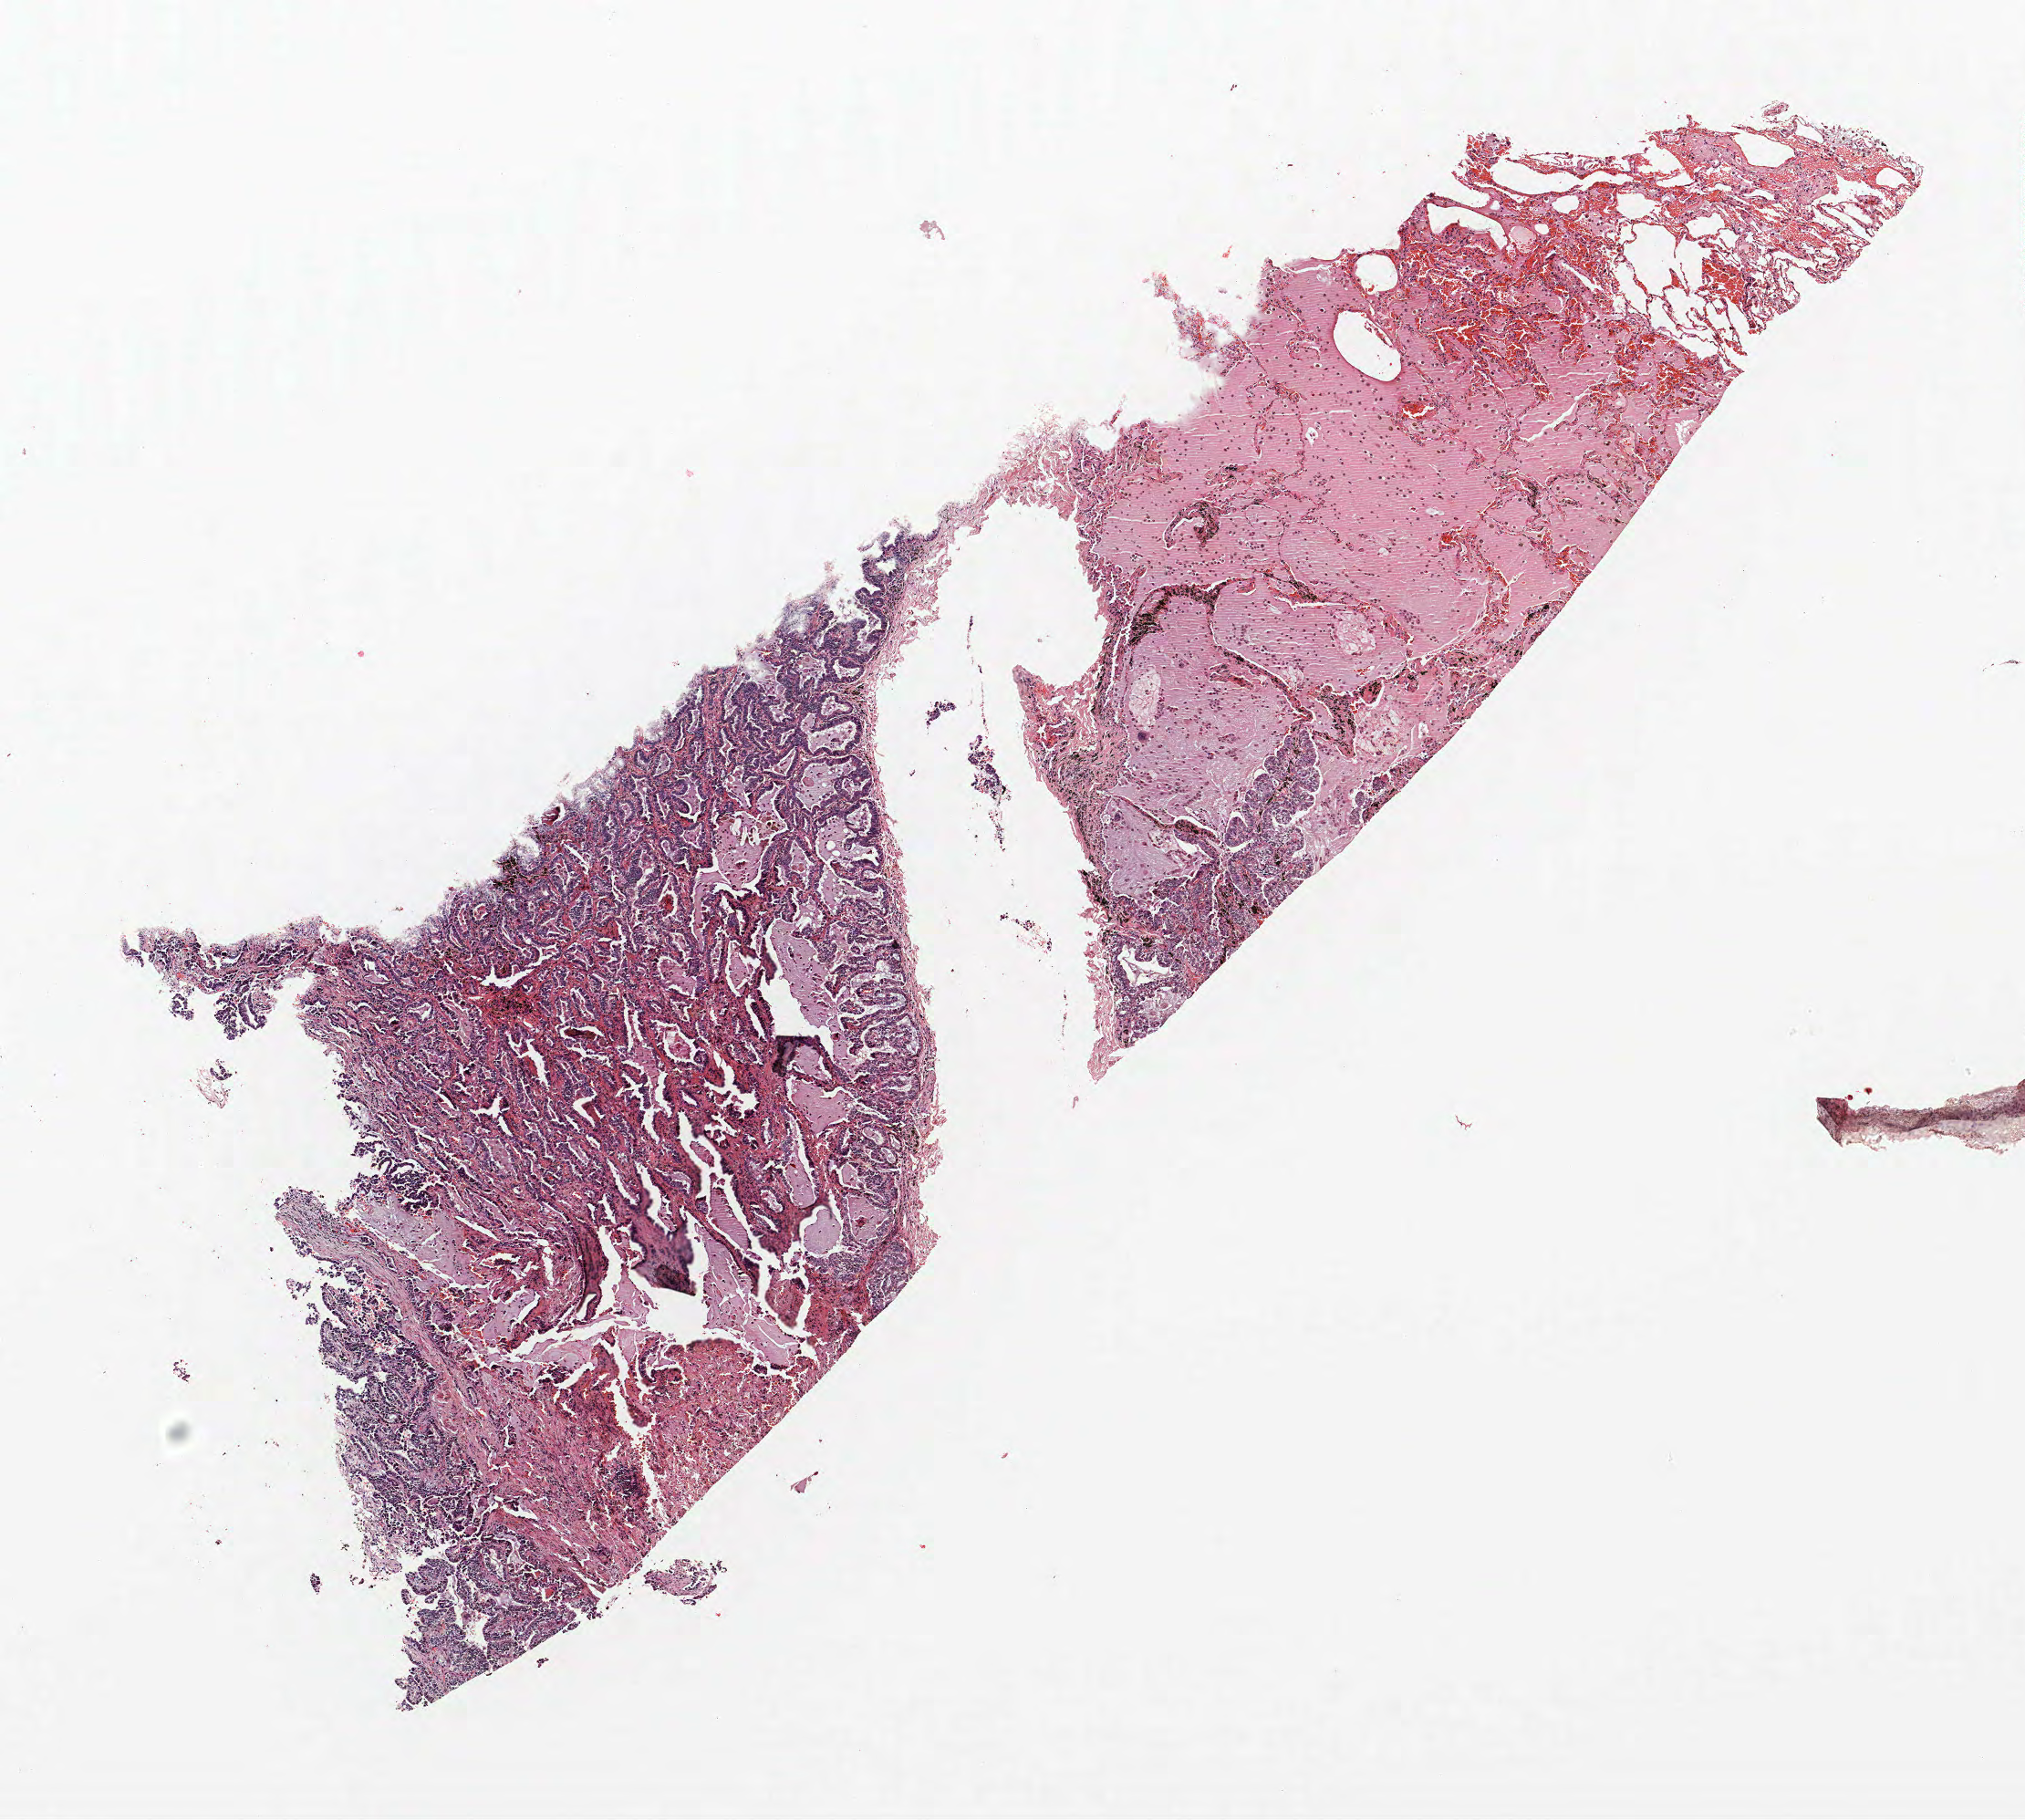
Whole-slide histology image, H&E, a low-resolution overview of the entire scanned area, about 8.9 x 8.0 mm, FFPE section, lung. Male patient, aged 58 at enrolment. Current smoker at enrolment. Grade: well differentiated (G1).
- primary tumour location (clinical record): left upper lobe
- participant's lung-cancer diagnosis: Bronchiolo-alveolar adenocarcinoma, NOS
- stage (AJCC 6th edition): IA
- tumour size (pathology): 17 mm